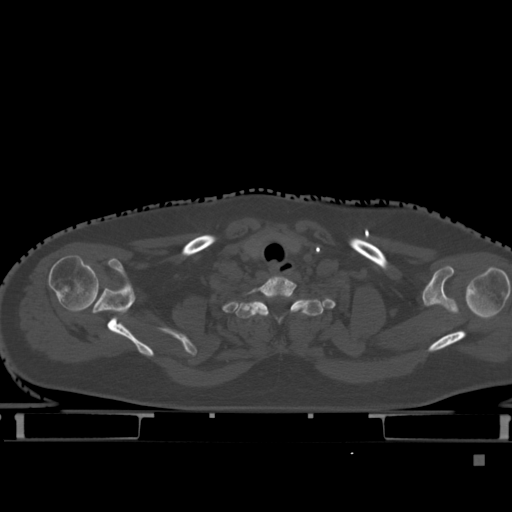
CT including the spine, one axial slice; slice 375 of 495 in the series (ordered by position); bone window (W 1800 / L 400 HU); 1.5 mm slice thickness; 512 × 512 image matrix, field of view 404 × 404 mm. Patient: female, 33 years. Case-level facts recorded for this patient, not image findings: primary cancer: breast; vertebrae with lytic lesions (as recorded): T1.
Outlined on this slice (semi-automatically segmented with operator editing):
- T1 vertebra: bounding box [x1, y1, x2, y2] px = [236, 291, 323, 325]